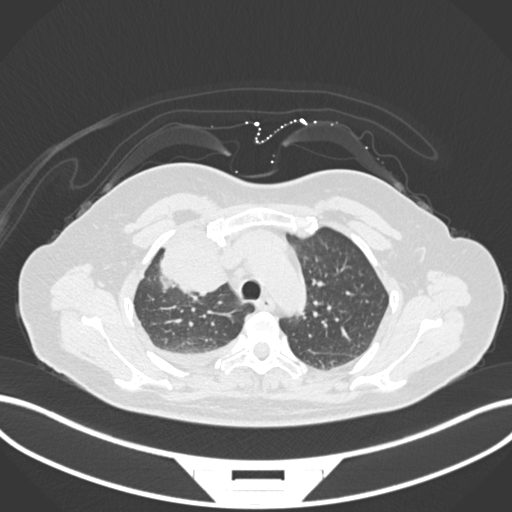
Chest CT, one axial slice; position 122 of 172 along the scan axis; reconstruction kernel B30f; lung window (W 1500 / L -600 HU); 1 mm slice thickness; 512 × 512 image matrix, field of view 400 × 400 mm. Female patient, age 52 years. From the clinical record (not read from this slice): clinical TNM (as recorded): T3 N1 M1.
Annotated regions visible in this slice (rectangle marked by the reading radiologist):
- lung tumour (recorded histology: adenocarcinoma): bounding box (x1, y1, x2, y2) in pixels: (149, 225, 227, 296)